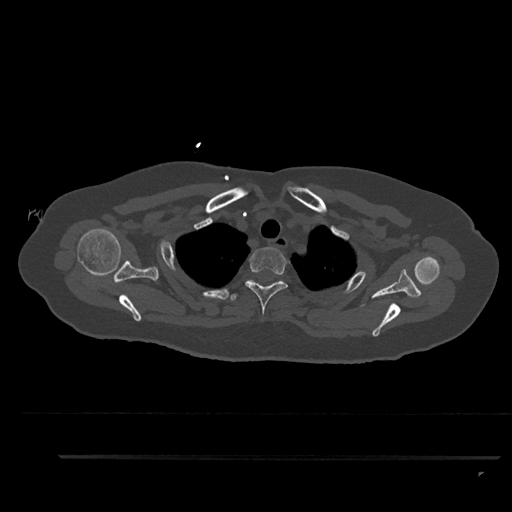
CT including the spine, one axial slice. Position 718 of 797 along the scan axis. Reconstruction kernel Br40s/3. Bone window (W 1800 / L 400 HU). 0.5 mm slice thickness. 512 × 512 image matrix, field of view 408 × 408 mm. Female patient, age 44 years. From the clinical record (not read from this slice): primary cancer: renal; vertebrae with lytic lesions (as recorded): L1.
Annotated regions visible in this slice (semi-automatically segmented with operator editing):
- T2 vertebra: bounding box (x1, y1, x2, y2) in pixels: (245, 247, 290, 316)
- T3 vertebra: (227, 280, 254, 301)